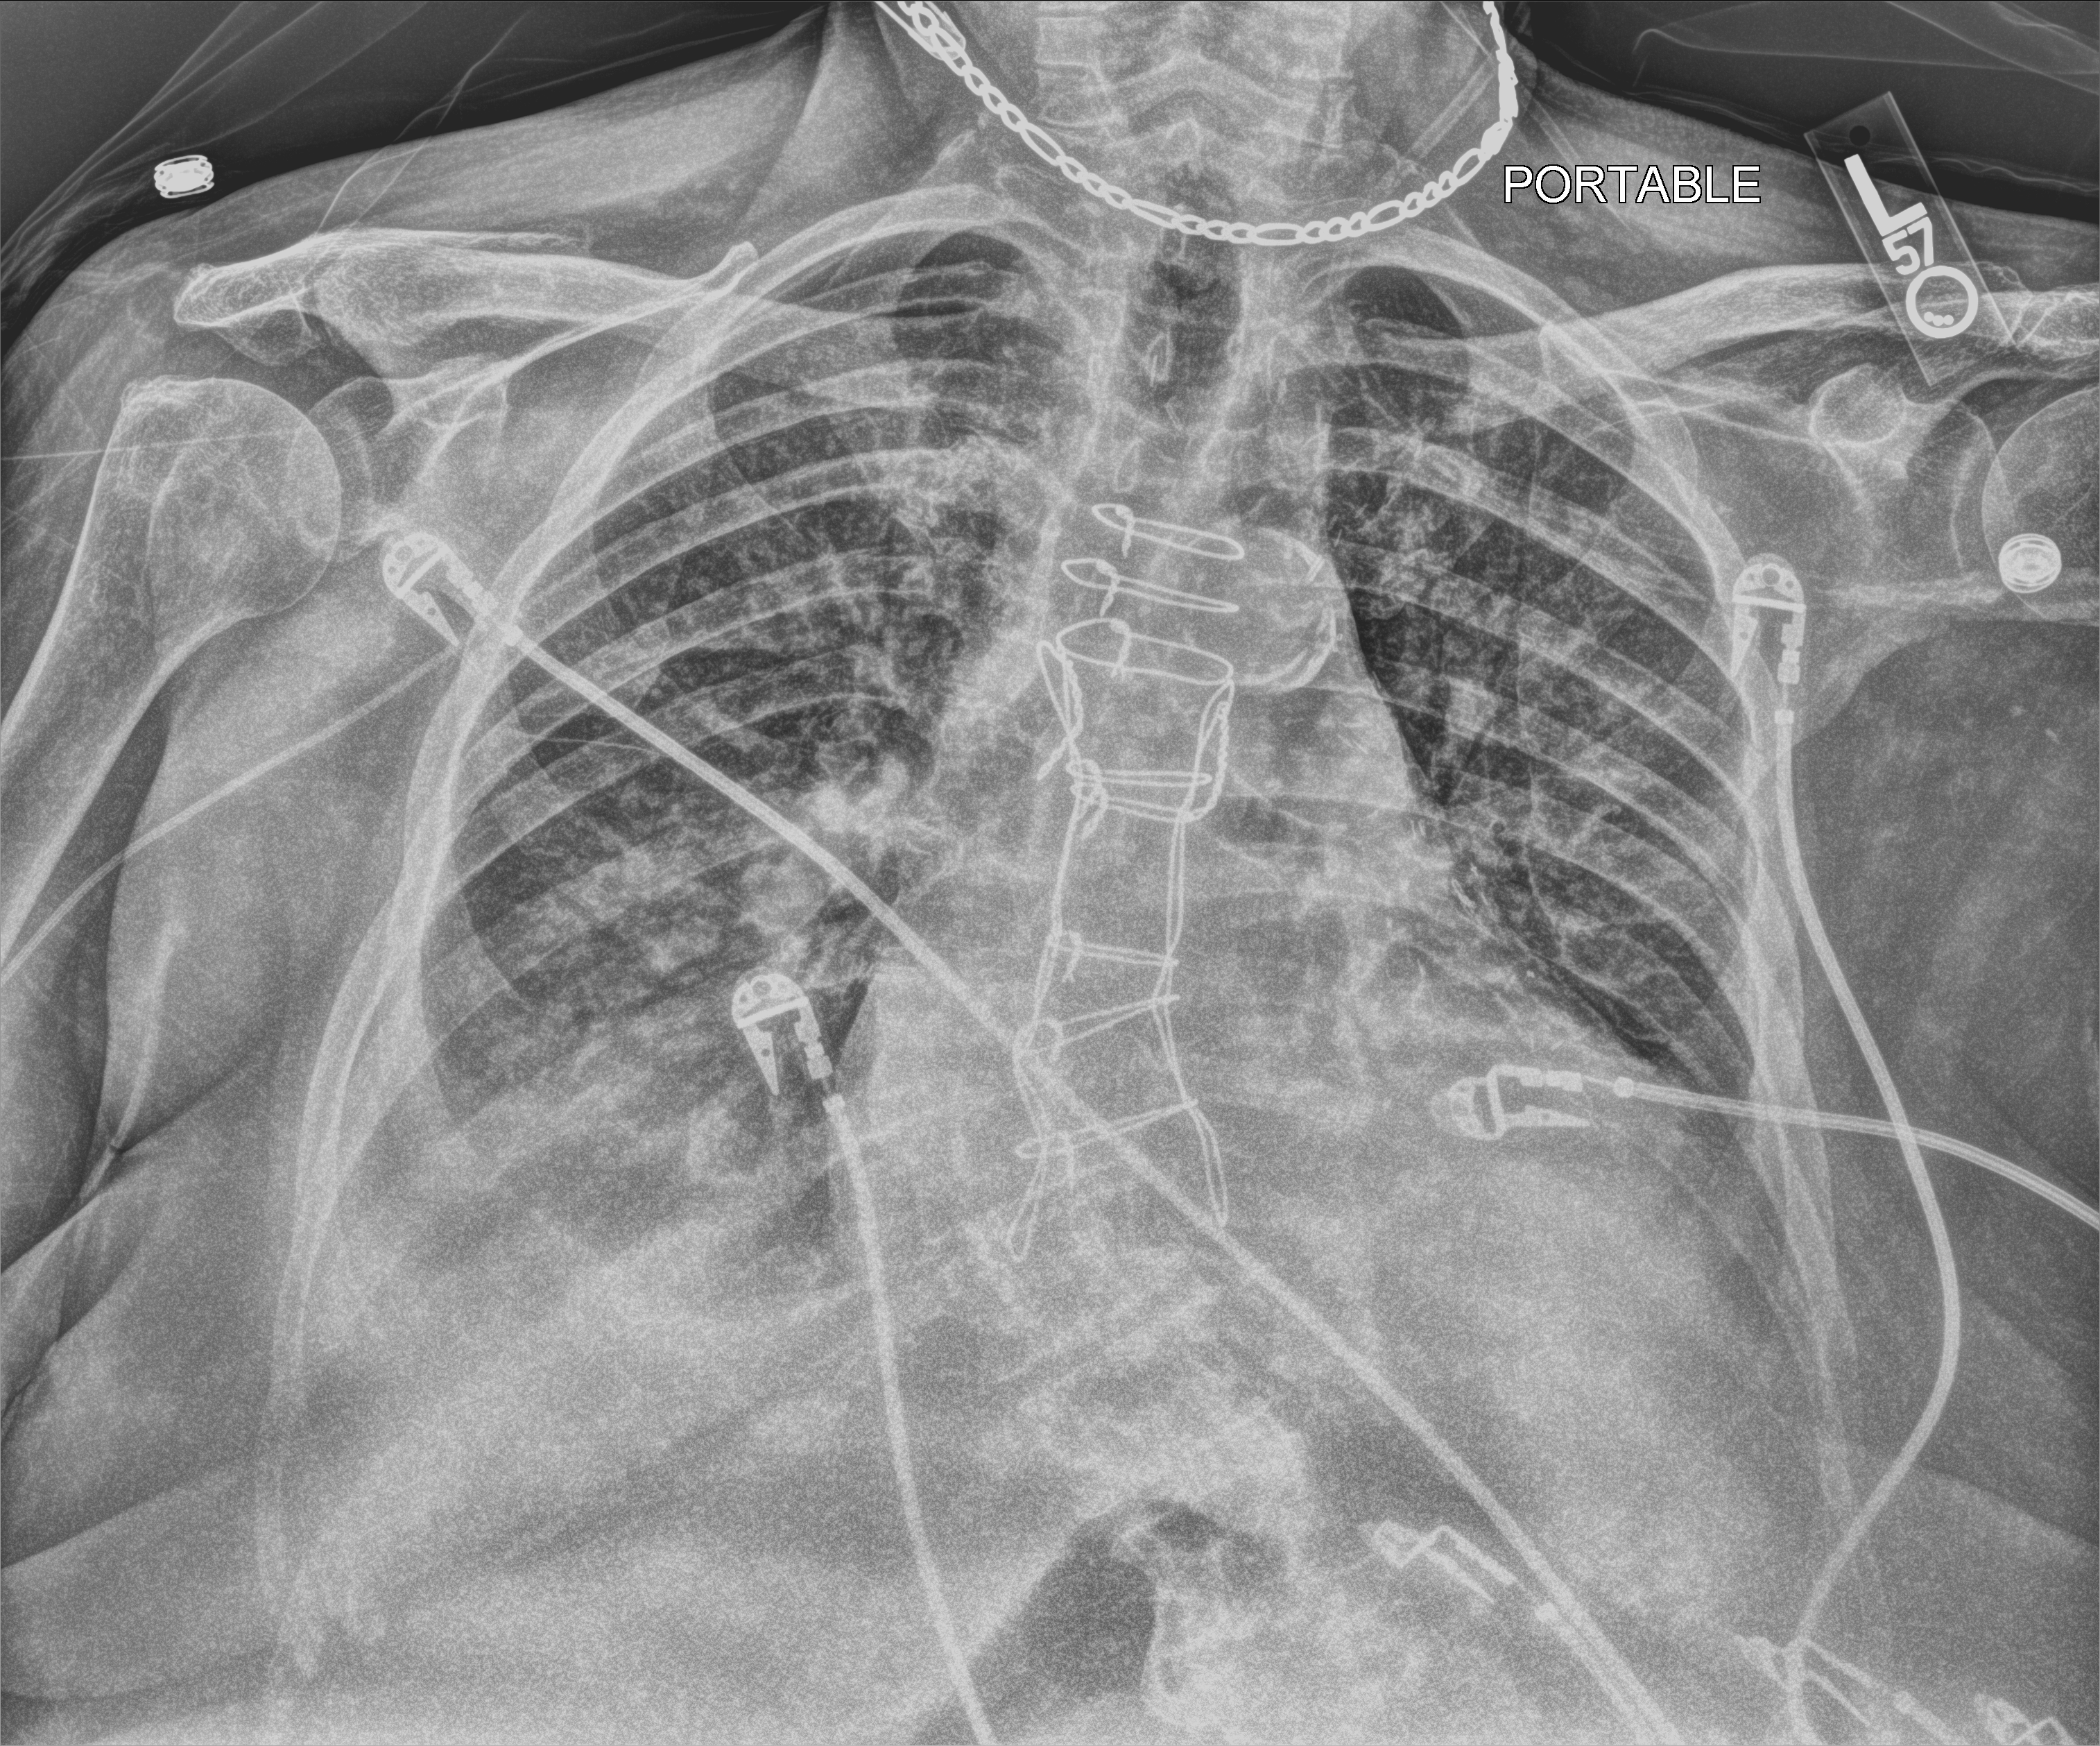
Chest X-ray (portable), anteroposterior (AP) projection. Patient hospitalised with COVID-19; female, aged 75–90 years.
Hospital-stay facts (about this admission, not read from this image; timing relative to this image not recorded): length of hospital stay: 10 days.